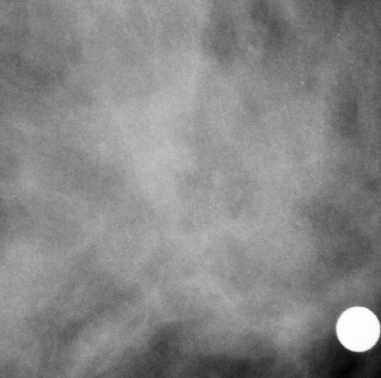
Crop from a digitized film mammogram around one marked abnormality; left breast; MLO view; BI-RADS breast density category 2 (scale 1–4).
- Mass, shape lobulated, margins ill defined; BI-RADS assessment category 4; subtlety rating 3 on a 1 (subtle) to 5 (obvious) scale; pathology (as recorded): malignant.